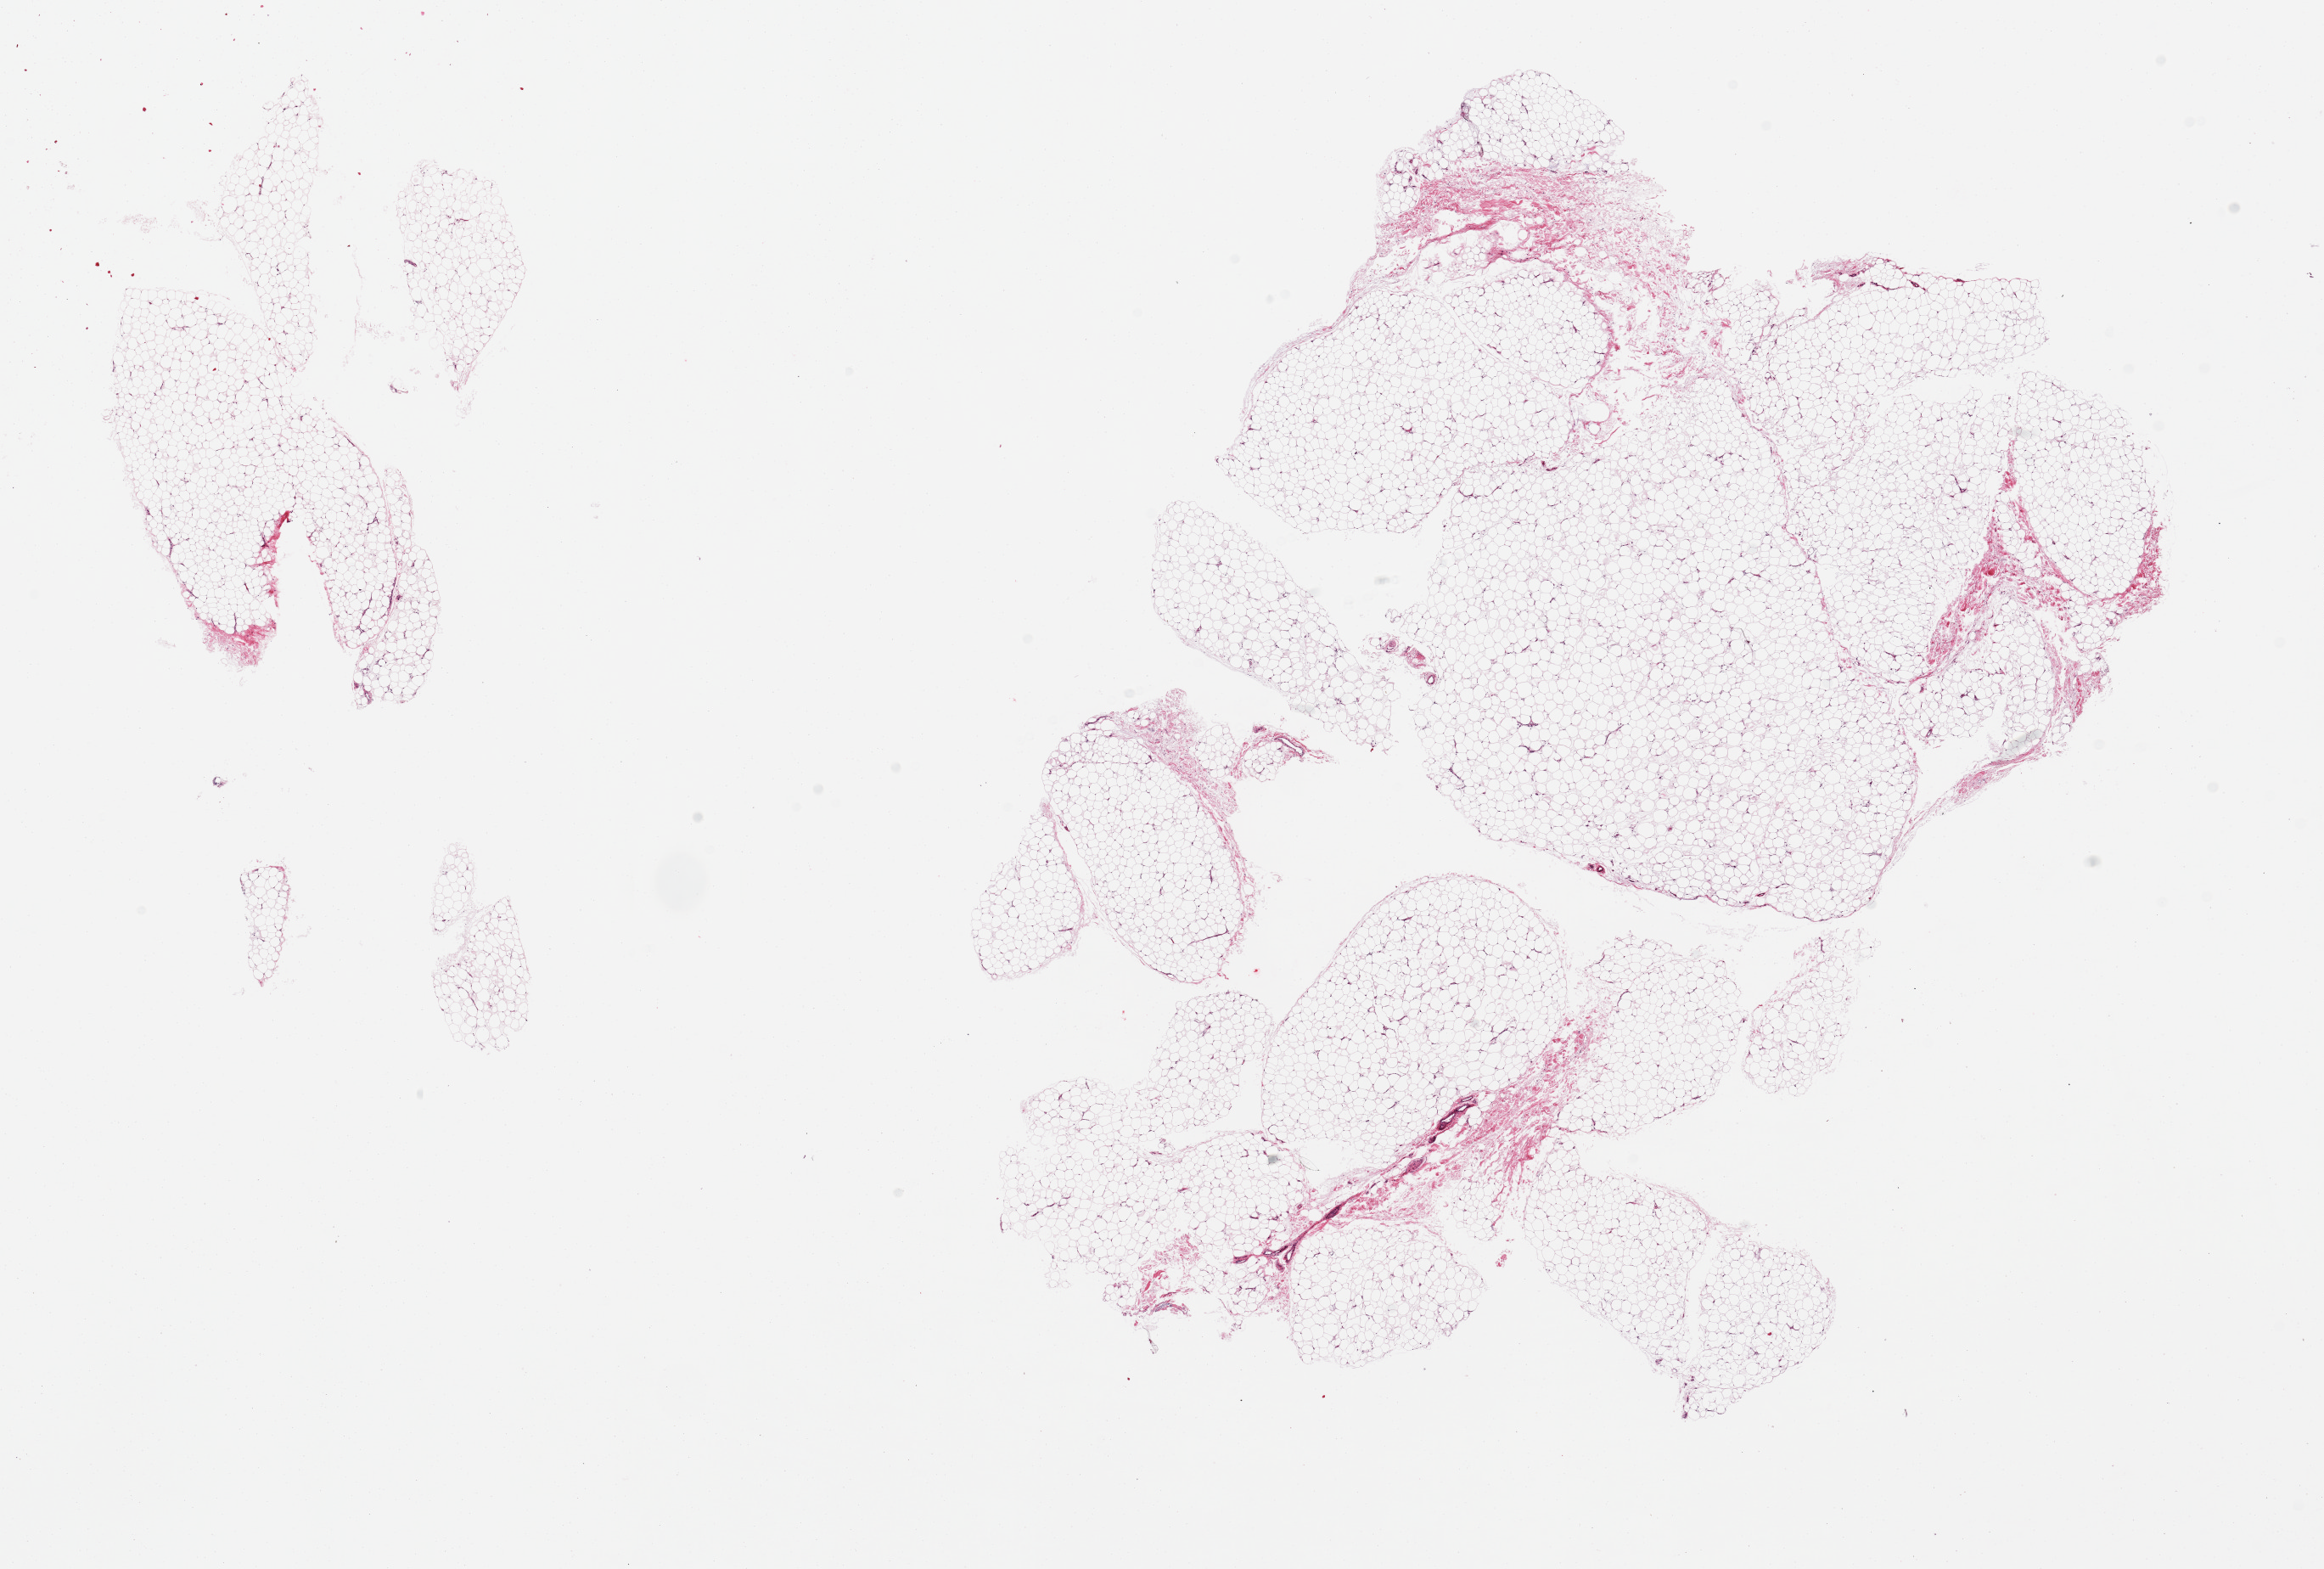
Whole-slide image, hematoxylin and eosin (H&E) stain, low-resolution overview of the scanned area, about 21.7 x 14.6 mm (acquisition: 20x scan). PAXgene-fixed, paraffin-embedded tissue. Target tissue: adipose tissue. Tissue donor sample. Donor: male.
- reviewer comment on this tissue sample: 2 fragmented pieces; ~10% fibrovascular component